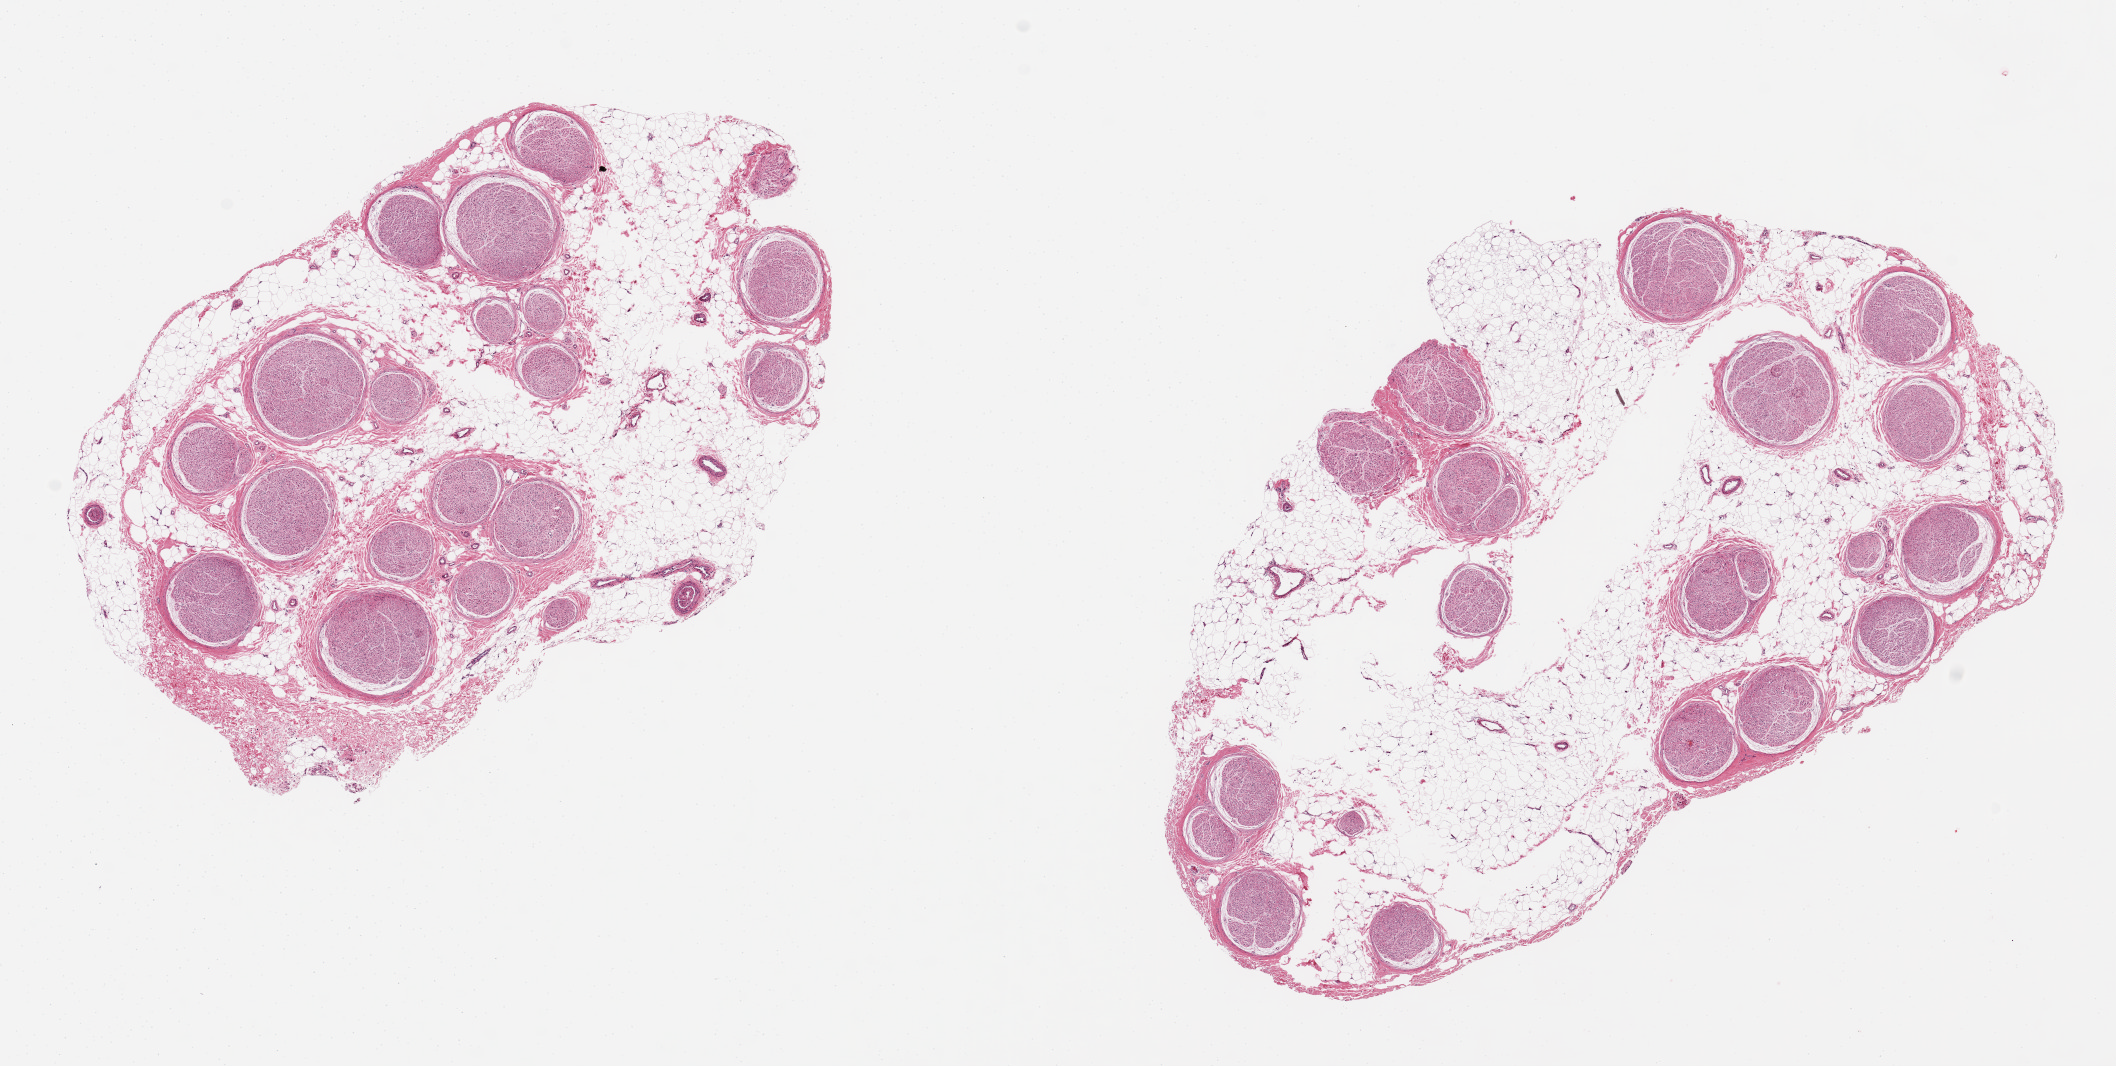
Whole-slide image, hematoxylin and eosin (H&E) stain — low-resolution overview of the scanned area, about 16.7 x 8.4 mm, PAXgene-fixed paraffin-embedded (PFPE) section, sampled site (target tissue): tibial nerve, tissue donor sample. Donor sex: male.
- reviewer comment on this tissue sample: 2 ~7.5x4mm aliquots, nerve bundles widely dispersed; ~ 70% both aliquots is interstitial fat